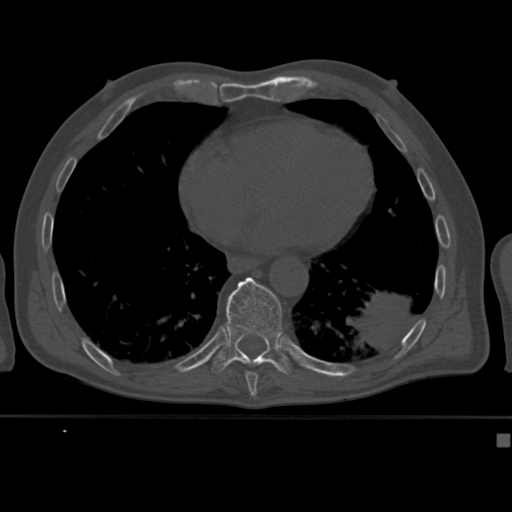
CT including the spine, one axial slice; slice 234 of 430 in the series (ordered by position); 120 kVp; bone window (W 1800 / L 400 HU); 1.5 mm slice thickness; 512 × 512 image matrix. Male patient, age 64 years. From the clinical record (not read from this slice): primary cancer: uterus; vertebrae with lytic lesions (as recorded): T1, T4, T5, T7, L5.
Annotated regions visible in this slice (semi-automatic segmentation, software-assisted and operator-edited):
- T10 vertebra: bounding box (x1, y1, x2, y2) in pixels: (211, 277, 294, 375)
- T9 vertebra: (245, 371, 259, 382)